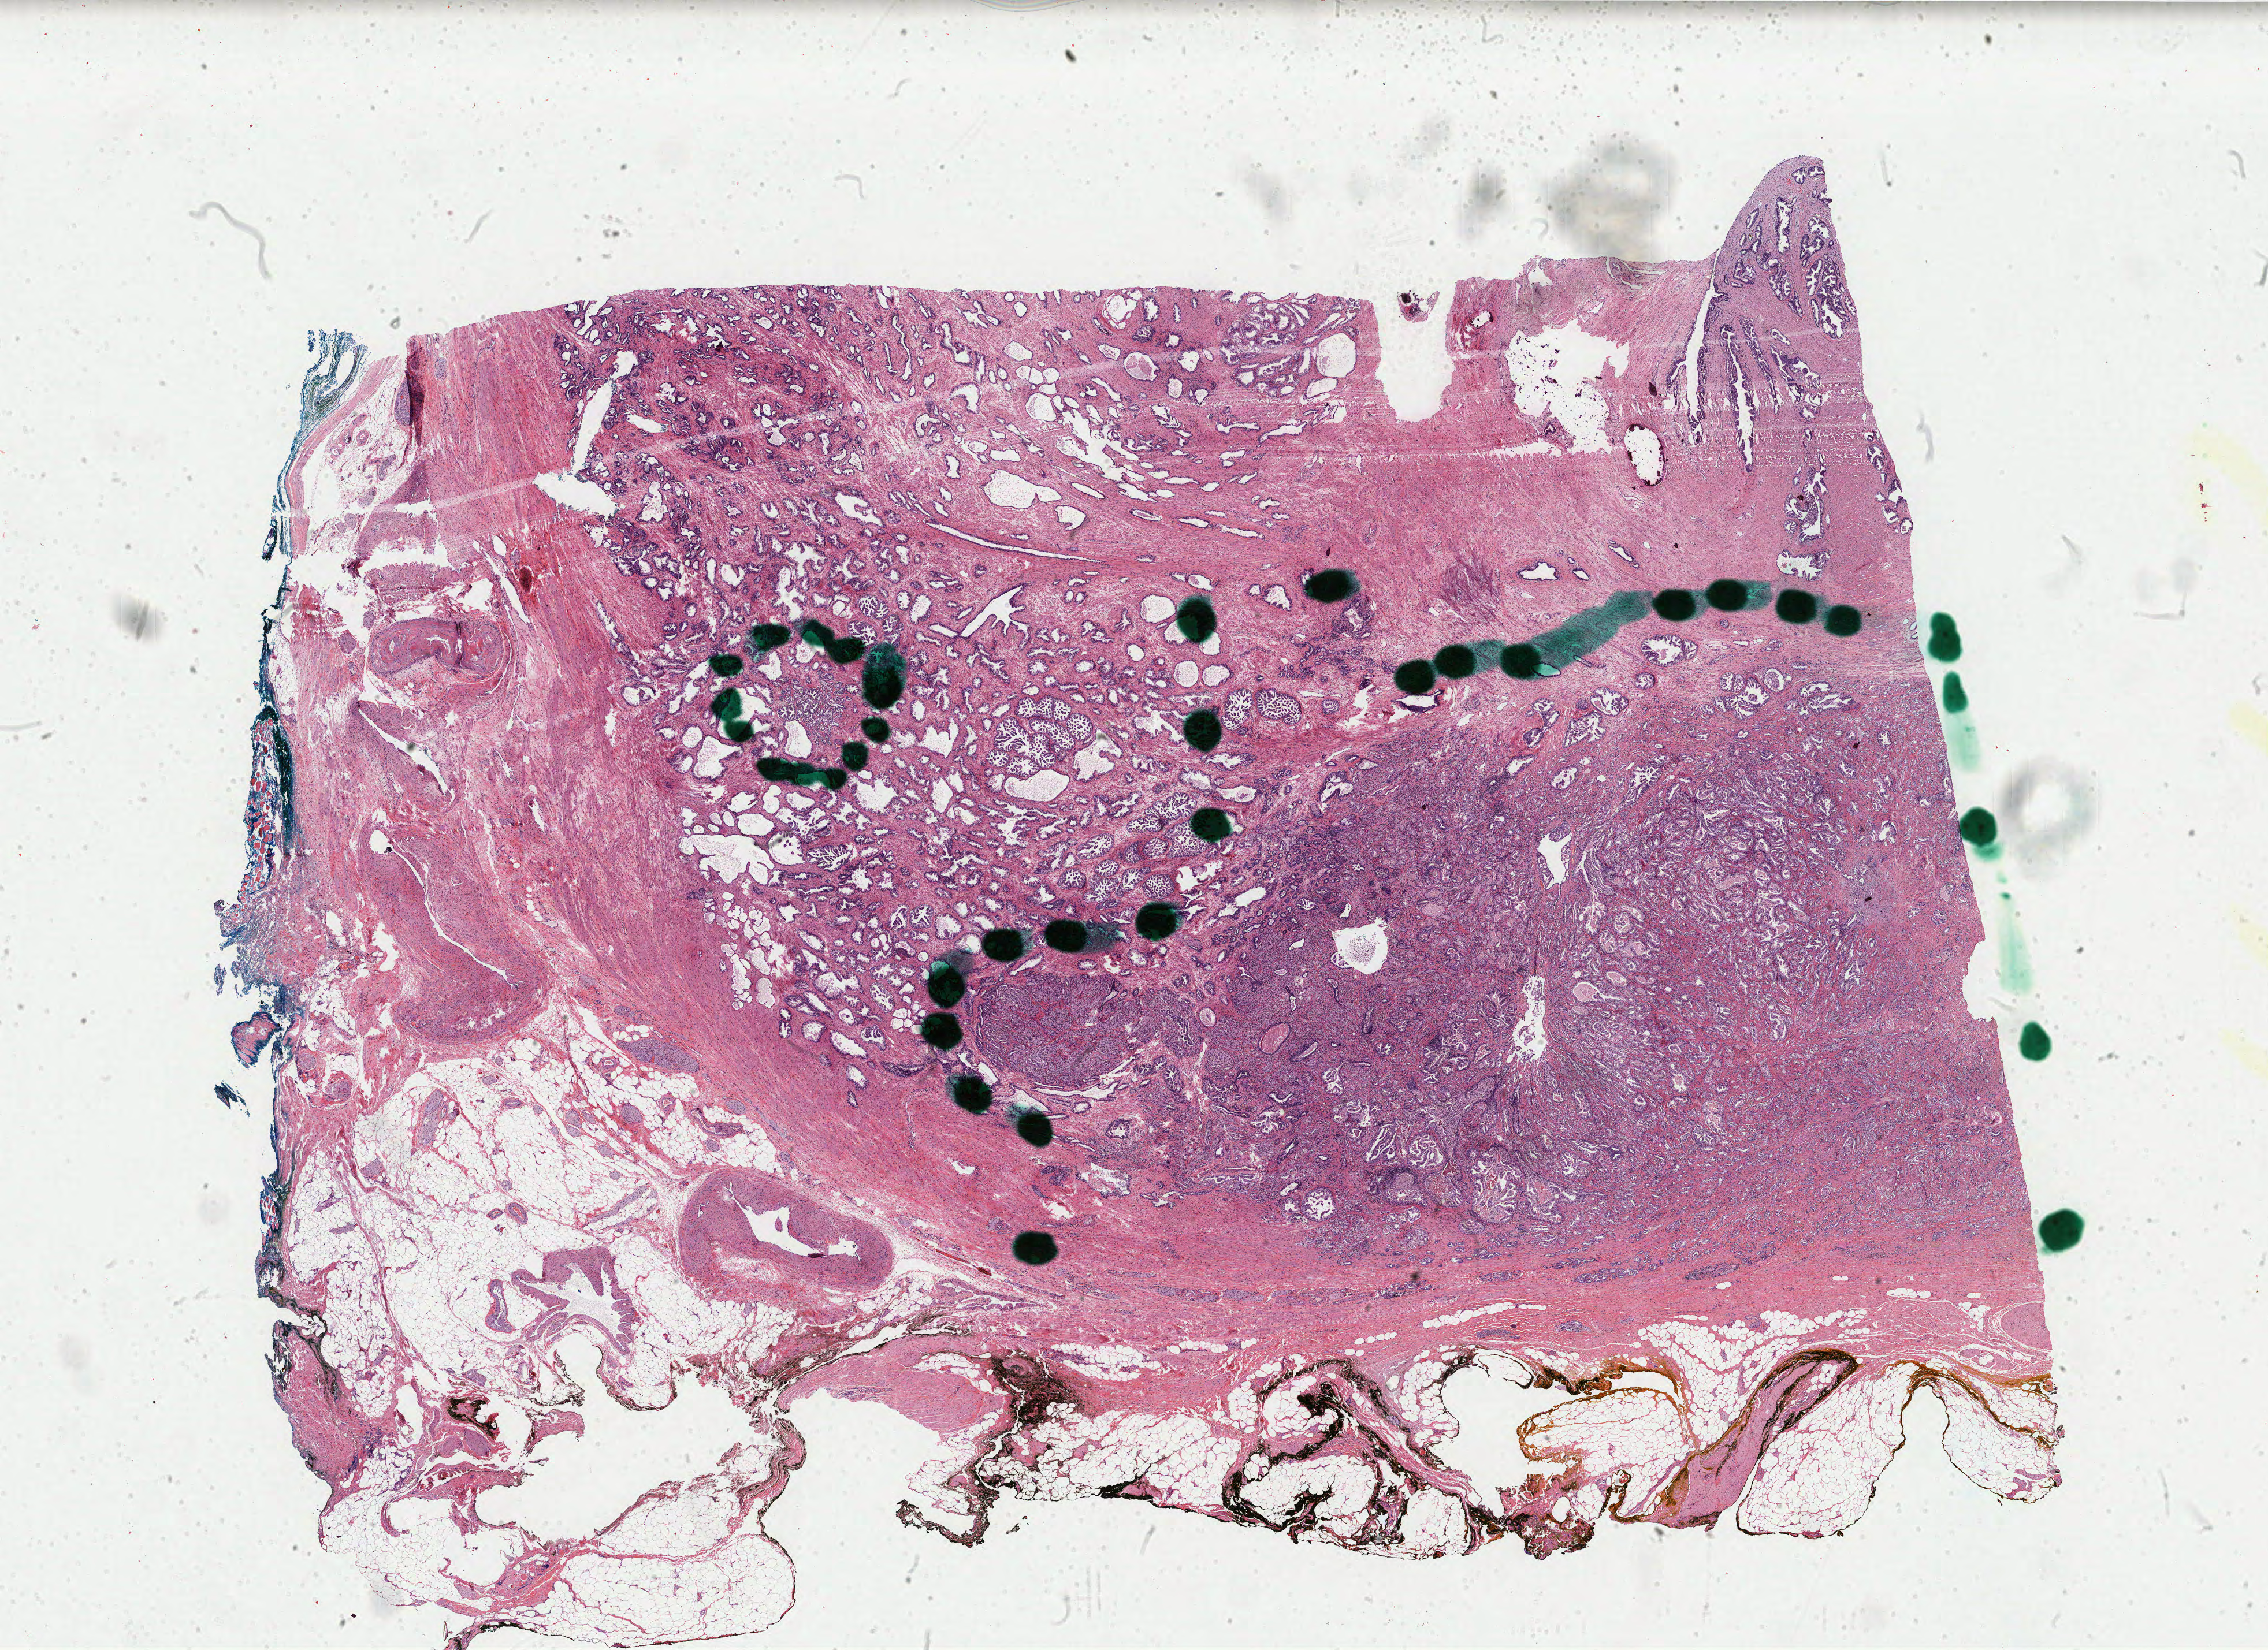
Digitized H&E-stained tissue section (whole slide), shown as a low-resolution overview of the whole scanned area (about 31.2 x 22.7 mm, slide scanned at 40x), formalin-fixed paraffin-embedded (FFPE) diagnostic section, sample: primary tumour, prostate. Male patient; age at initial diagnosis 60 years. Gleason score: 7 (4+3).
* lymph nodes positive (case pathology): 0 of 8 examined
* histologic diagnosis: Adenocarcinoma, NOS (prostate gland)